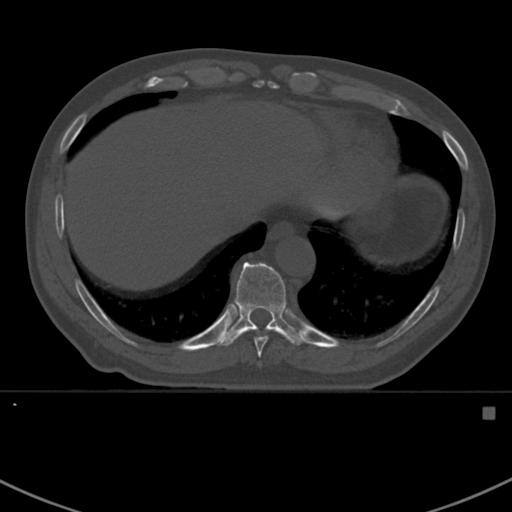
CT including the spine, one axial slice; slice 372 of 412 in the series (ordered by position); reconstruction kernel Br40s; 120 kVp; bone window (W 1800 / L 400 HU); 512 × 512 image matrix, field of view 358 × 358 mm. Patient: male, 59 years. Case-level facts recorded for this patient, not image findings: primary cancer: prostate.
Structures marked on this image (semi-automatic segmentation, software-assisted and operator-edited):
- T10 vertebra: bounding box (x1, y1, x2, y2) in pixels: (216, 262, 303, 346)
- T9 vertebra: (254, 336, 267, 358)